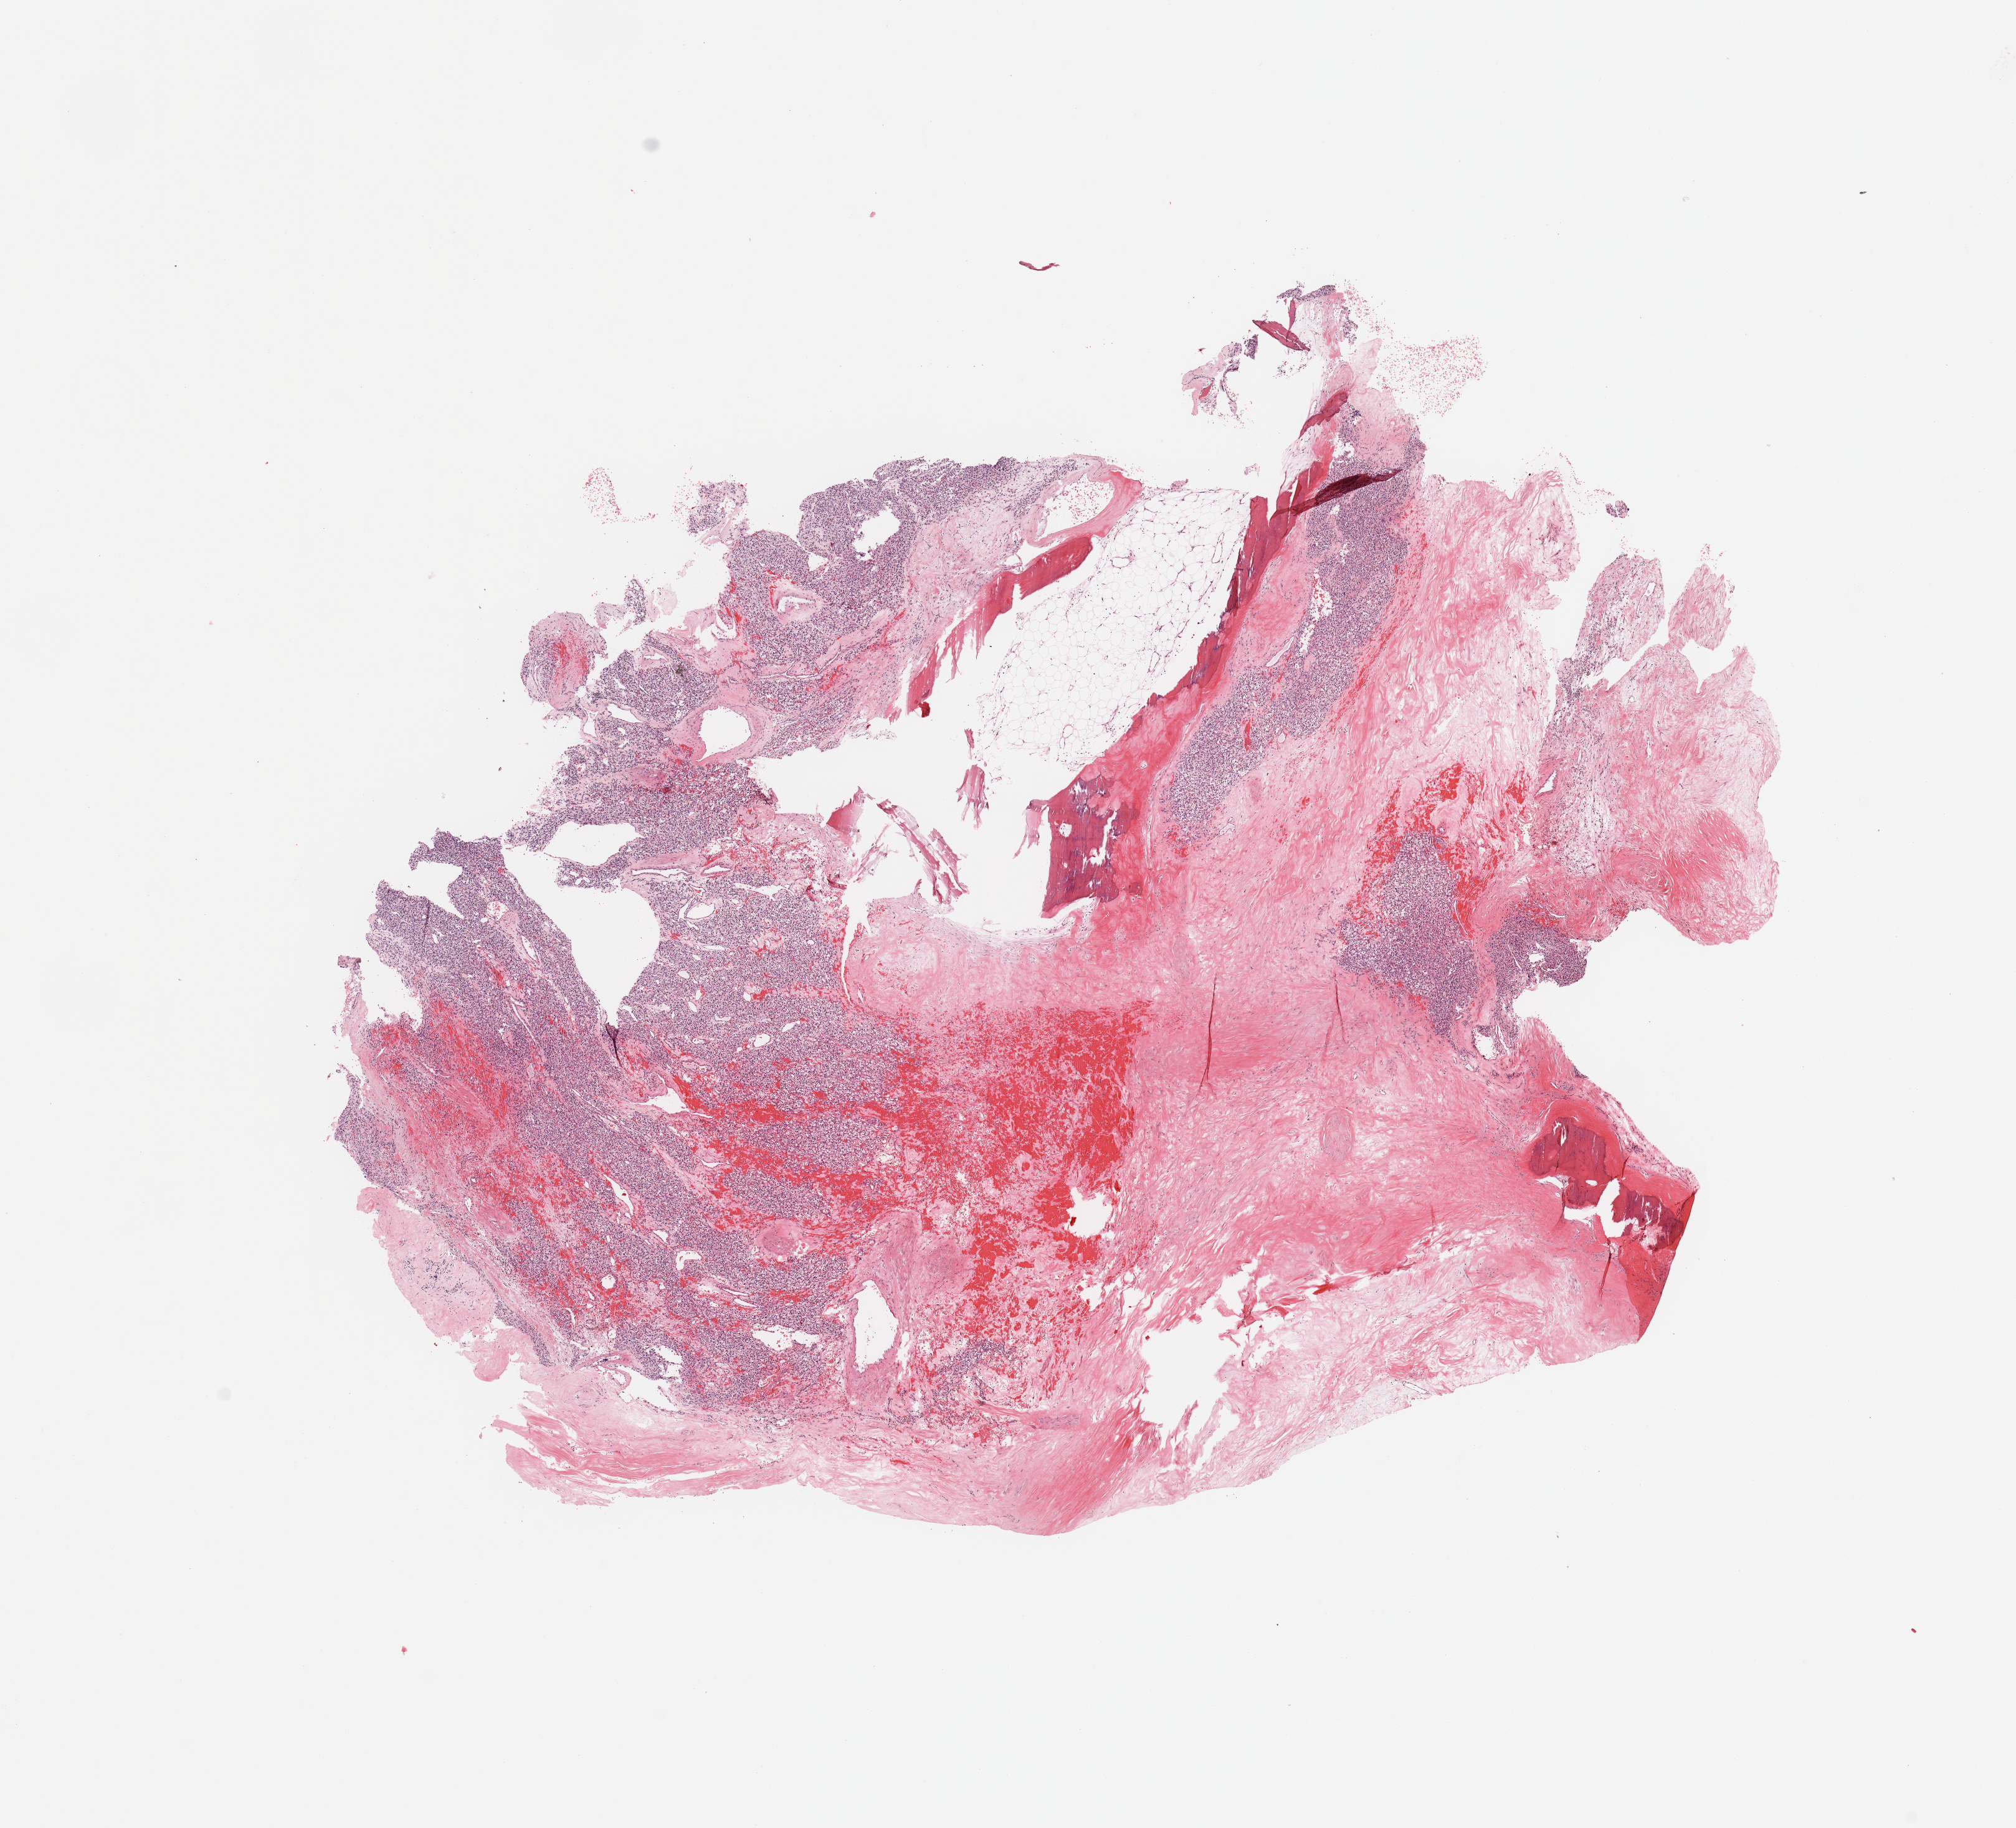
Digitized H&E-stained tissue section (whole slide) — low-resolution overview of the scanned area, about 12.8 x 11.6 mm (slide scanned at 20x); tumour tissue sample, sampled site: kidney. Female, 61 y/o. Histologic grade: G2 (moderately differentiated). Slide review estimates, as recorded: tumour nuclei 80%, necrosis 5%.
Primary tumour site (as recorded): lower pole. Diagnosis: Renal cell carcinoma, NOS. AJCC pathologic stage: I.